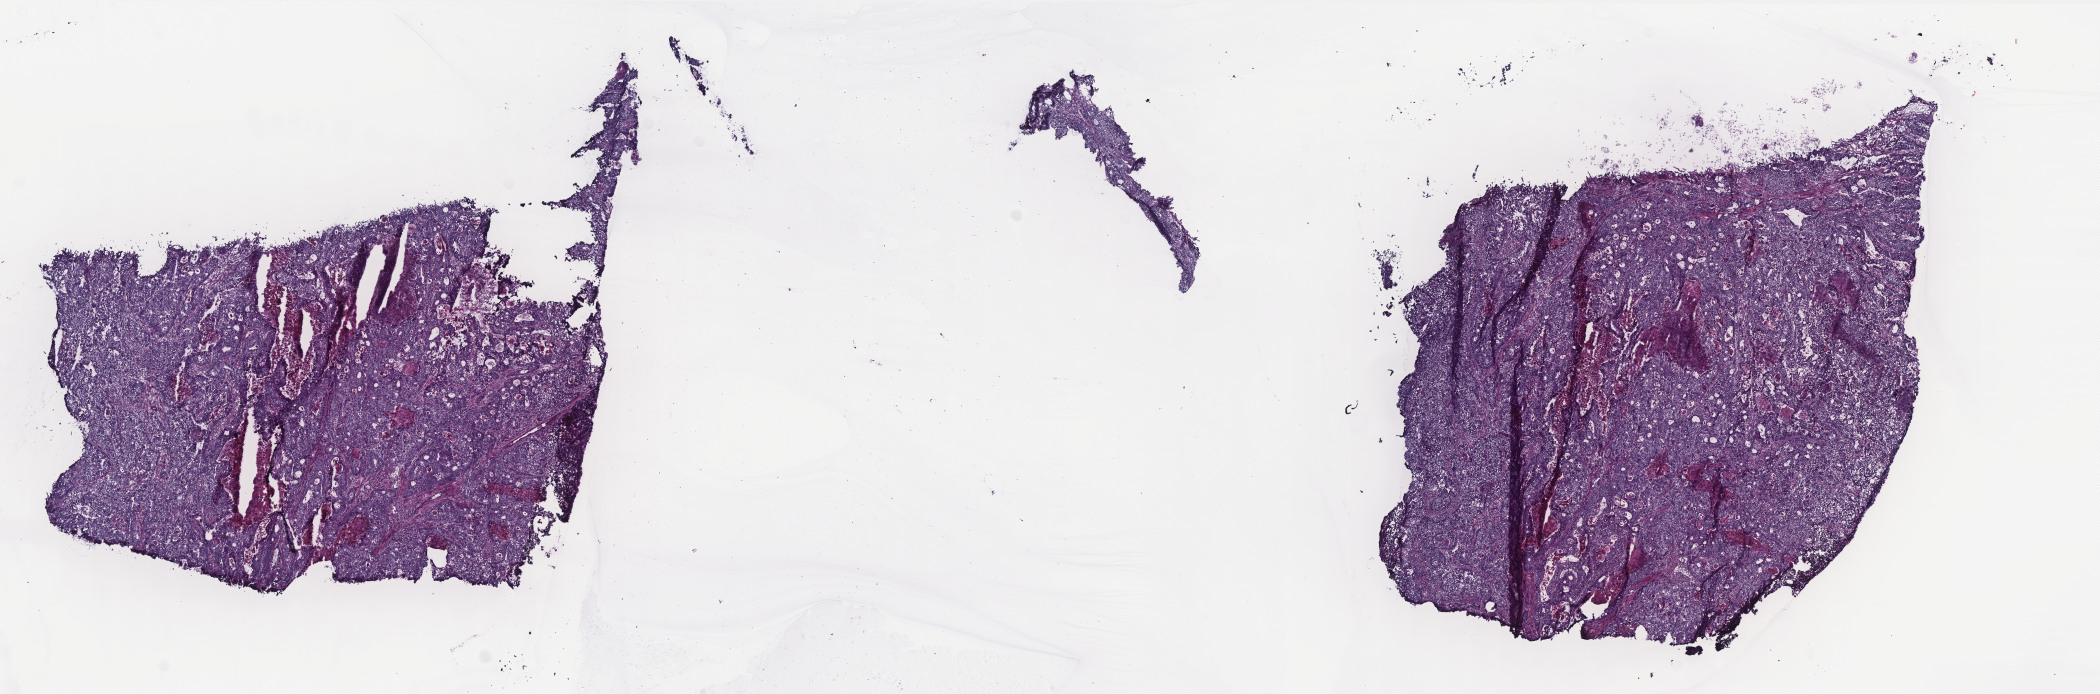
Whole-slide histology image, Hematoxylin and eosin (H&E) stained — low-resolution overview of the scanned area, about 16.8 x 5.6 mm (from a 40x scan). Frozen section. Primary tumour sample from the colon. Male, age 50 years at initial diagnosis. Slide review estimates, as recorded: tumour cells 85%, tumour nuclei 70%, normal cells 0%, stromal cells 5%, necrosis 10%. Inflammatory infiltration, as recorded: lymphocyte infiltration 3%, monocyte infiltration 2%, neutrophil infiltration 18%.
Lymph nodes positive (case pathology): 7 of 20 examined. Pathologic diagnosis: Adenocarcinoma, NOS (ascending colon). AJCC pathologic stage: IV (6th edition).